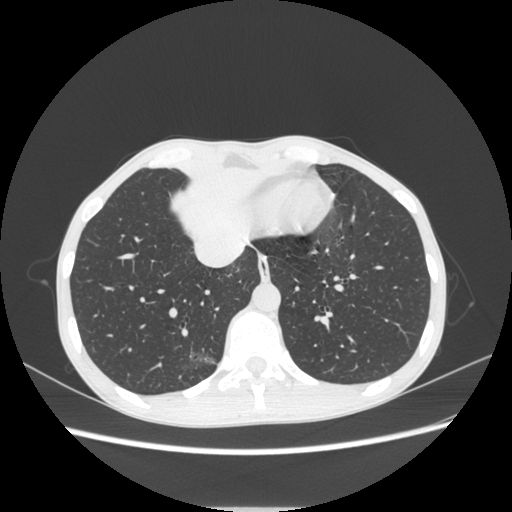
Chest CT, one axial slice; slice 80 of 272 in the series (ordered by position); reconstruction kernel STANDARD; 120 kVp; lung window (W 1500 / L -600 HU); 512 × 512 image matrix. Patient: female, 51 years. From the clinical record (not read from this slice): clinical TNM (as recorded): T1c N0 M0.
Annotated regions visible in this slice (bounding box drawn by a radiologist):
- lung tumour (recorded histology: adenocarcinoma): bounding box (x1, y1, x2, y2) in pixels: (180, 343, 222, 383)